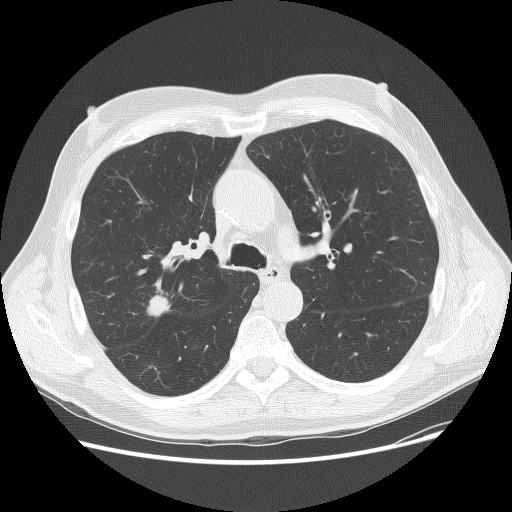
Chest CT (low-dose screening protocol), one axial image; baseline annual screen; lung window (W 1500 / L -600 HU); lung (sharp) reconstruction kernel (BONE); 120 kVp; 512 × 512 image matrix, field of view 380 × 380 mm. Male, age 70 years at enrolment.
Expert reader's lesion annotation, bounding box (x1, y1, x2, y2) in pixels: (134, 279, 197, 334). The screening reader recorded 2 non-calcified nodules or masses ≥4 mm on this exam (right upper lobe, left lower lobe); which of them this box marks is not recorded. Official screen result: positive, change unspecified: nodule(s) >= 4 mm or enlarging nodule(s), mass(es), or other non-specific abnormalities suspicious for lung cancer. Later outcome: lung cancer diagnosed 15 days after this screen — adenocarcinoma, NOS, right upper lobe, poorly differentiated (G3), stage IIA (AJCC 6th edition), 23 mm at pathology.